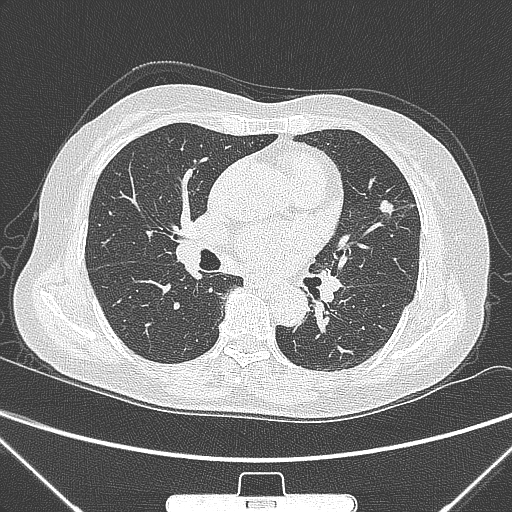
Chest CT, one axial slice; lung window (W 1500 / L -600 HU); 512 × 512 image matrix. Female patient, age 70 years. Case-level facts recorded for this patient, not image findings: clinical TNM (as recorded): T1b N0 M0.
Outlined on this slice (bounding box drawn by a radiologist):
- lung tumour (recorded histology: adenocarcinoma): bounding box [x1, y1, x2, y2] px = [375, 197, 400, 224]